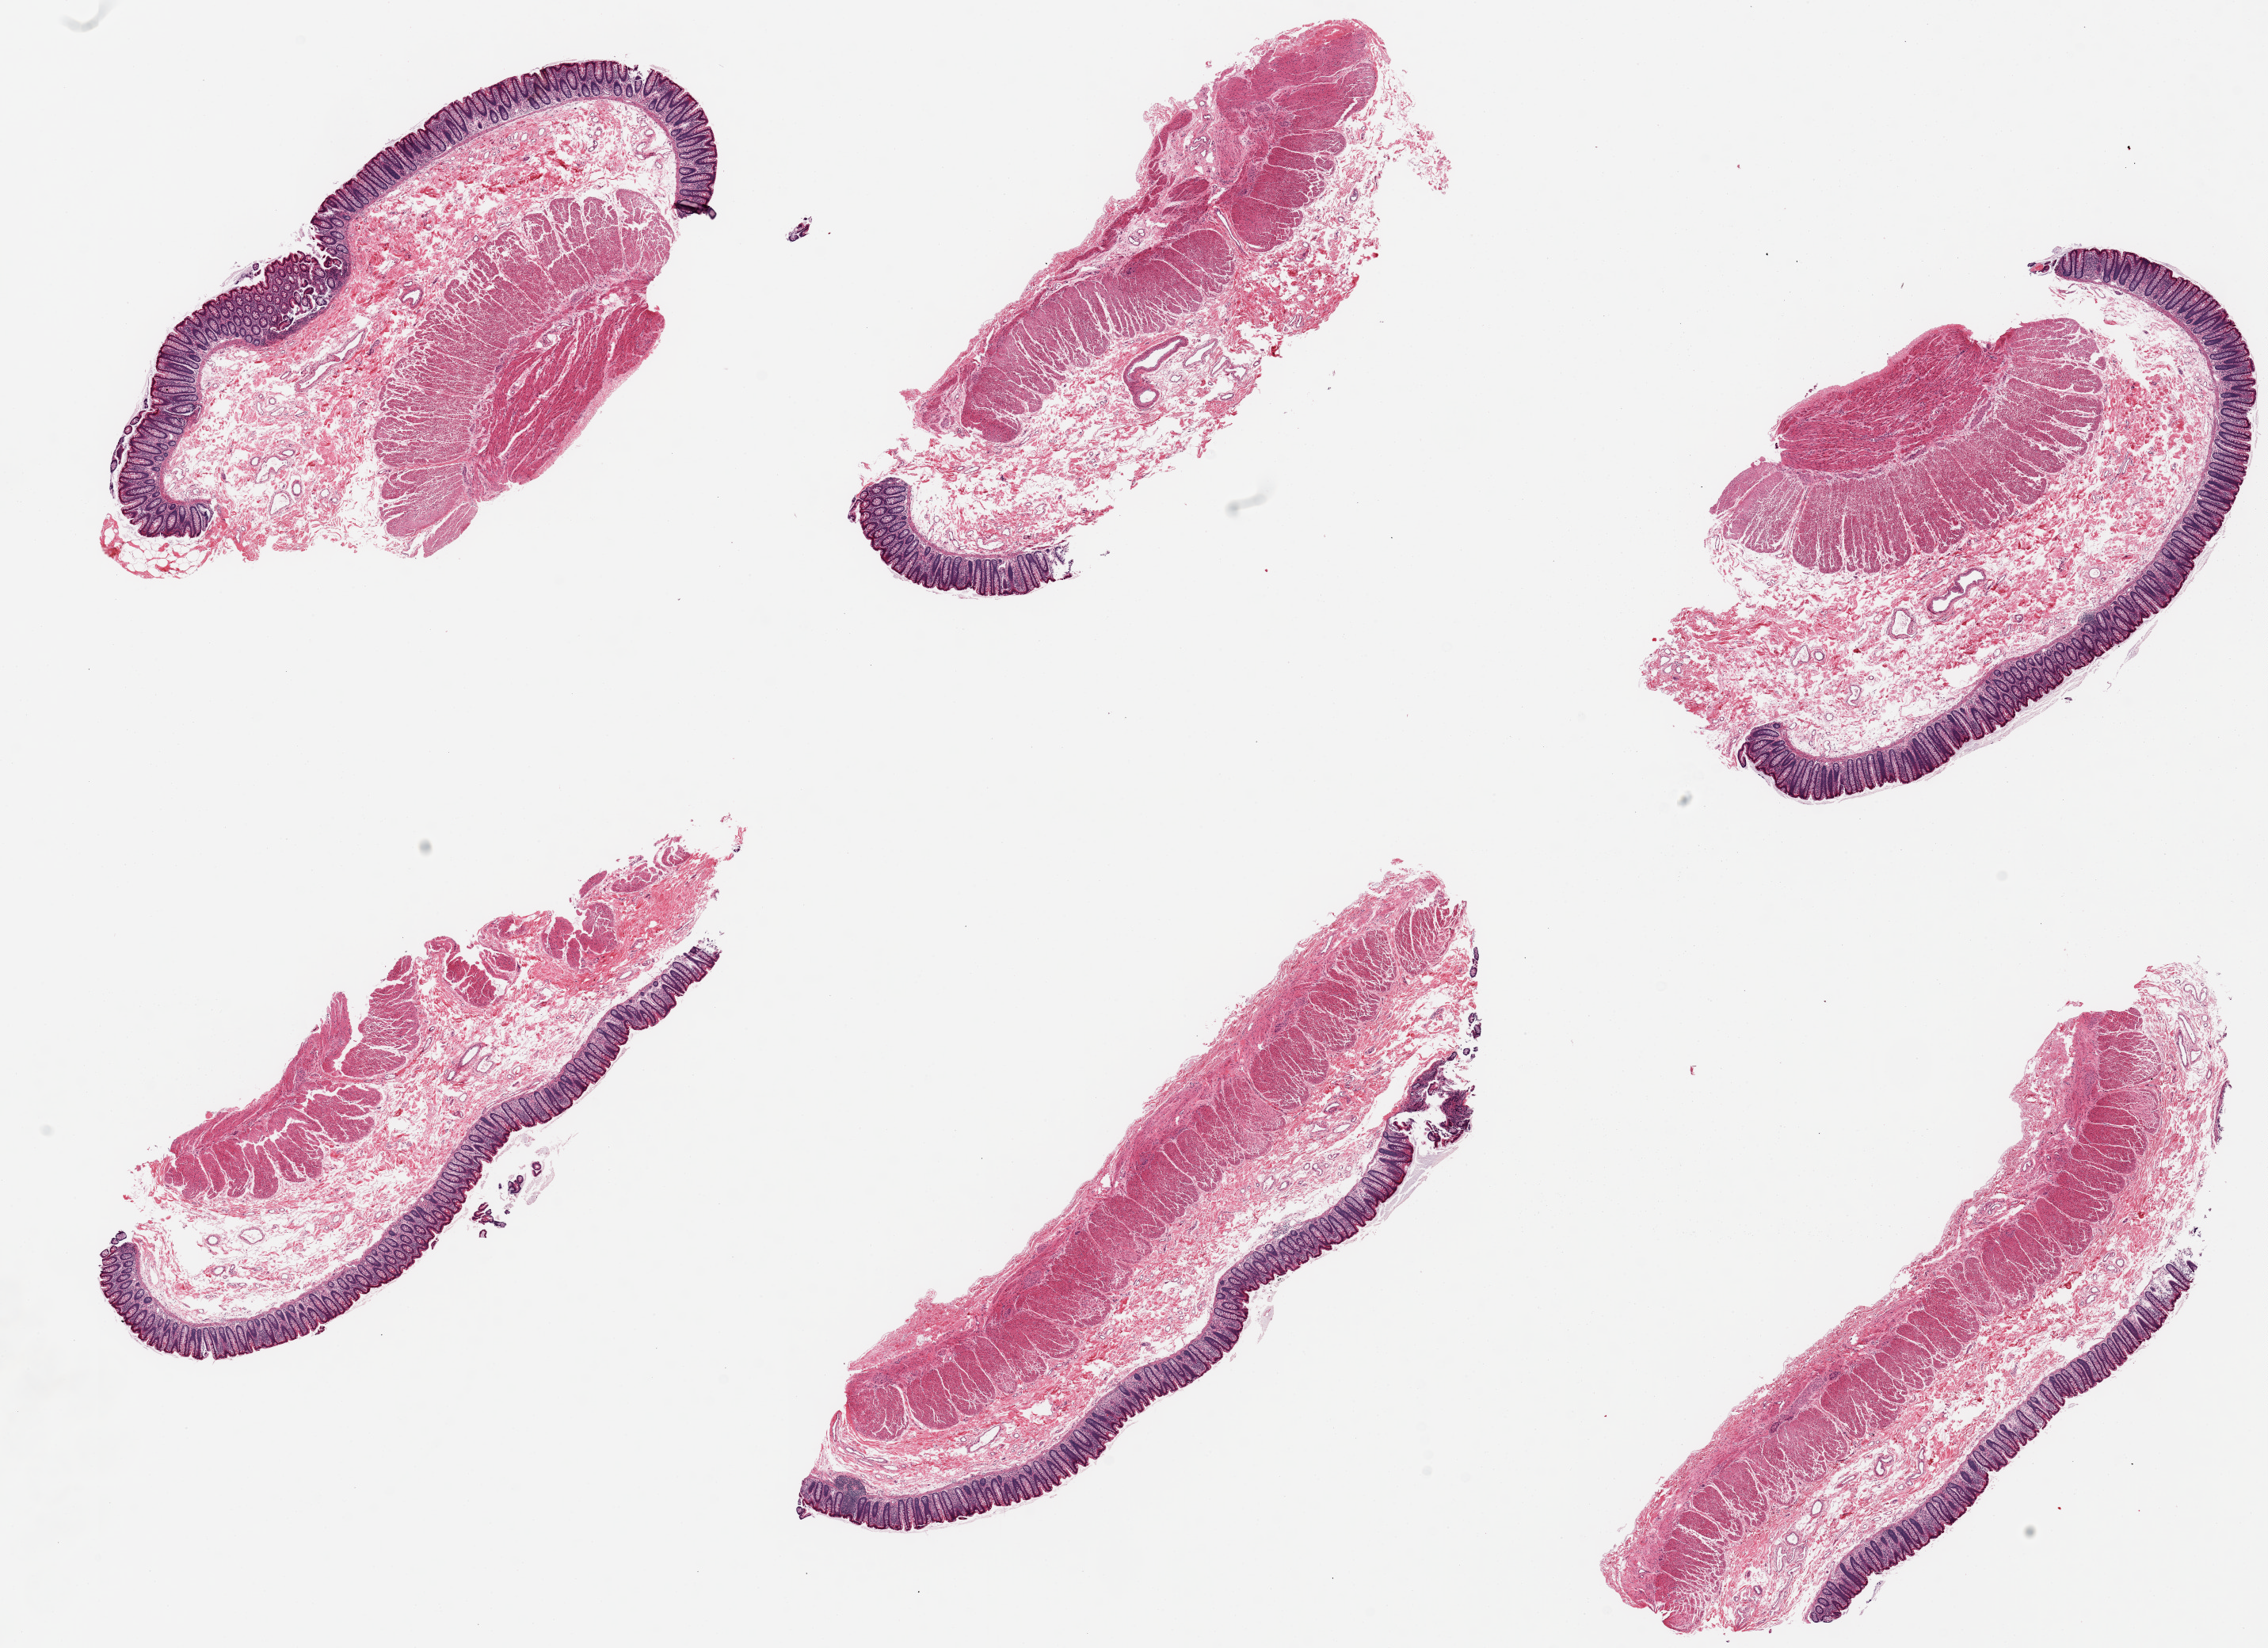
Whole-slide image, haematoxylin and eosin stain, brightfield — shown as a low-resolution overview of the whole scanned area (about 22.6 x 16.4 mm, from a 20x scan). PAXgene-fixed paraffin-embedded (PFPE) section. Target tissue: transverse colon. Donor tissue sample.
Reviewer comment on this tissue sample: 6 pieces; well dissected full thickness mucosa & muscle.